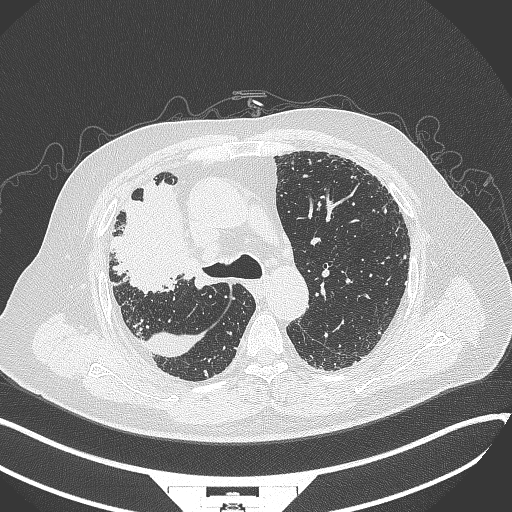
Chest CT, one axial slice. Slice 238 of 384 in the series (ordered by position). 120 kVp. Lung window (W 1500 / L -600 HU). 1 mm slice thickness. 512 × 512 image matrix, field of view 400 × 400 mm. Male patient, age 69 years. From the clinical record (not read from this slice): clinical TNM (as recorded): T4 N3 M1.
Annotated regions visible in this slice (rectangle marked by the reading radiologist):
- lung tumour (recorded histology: adenocarcinoma): bounding box (x1, y1, x2, y2) in pixels: (110, 180, 188, 300)